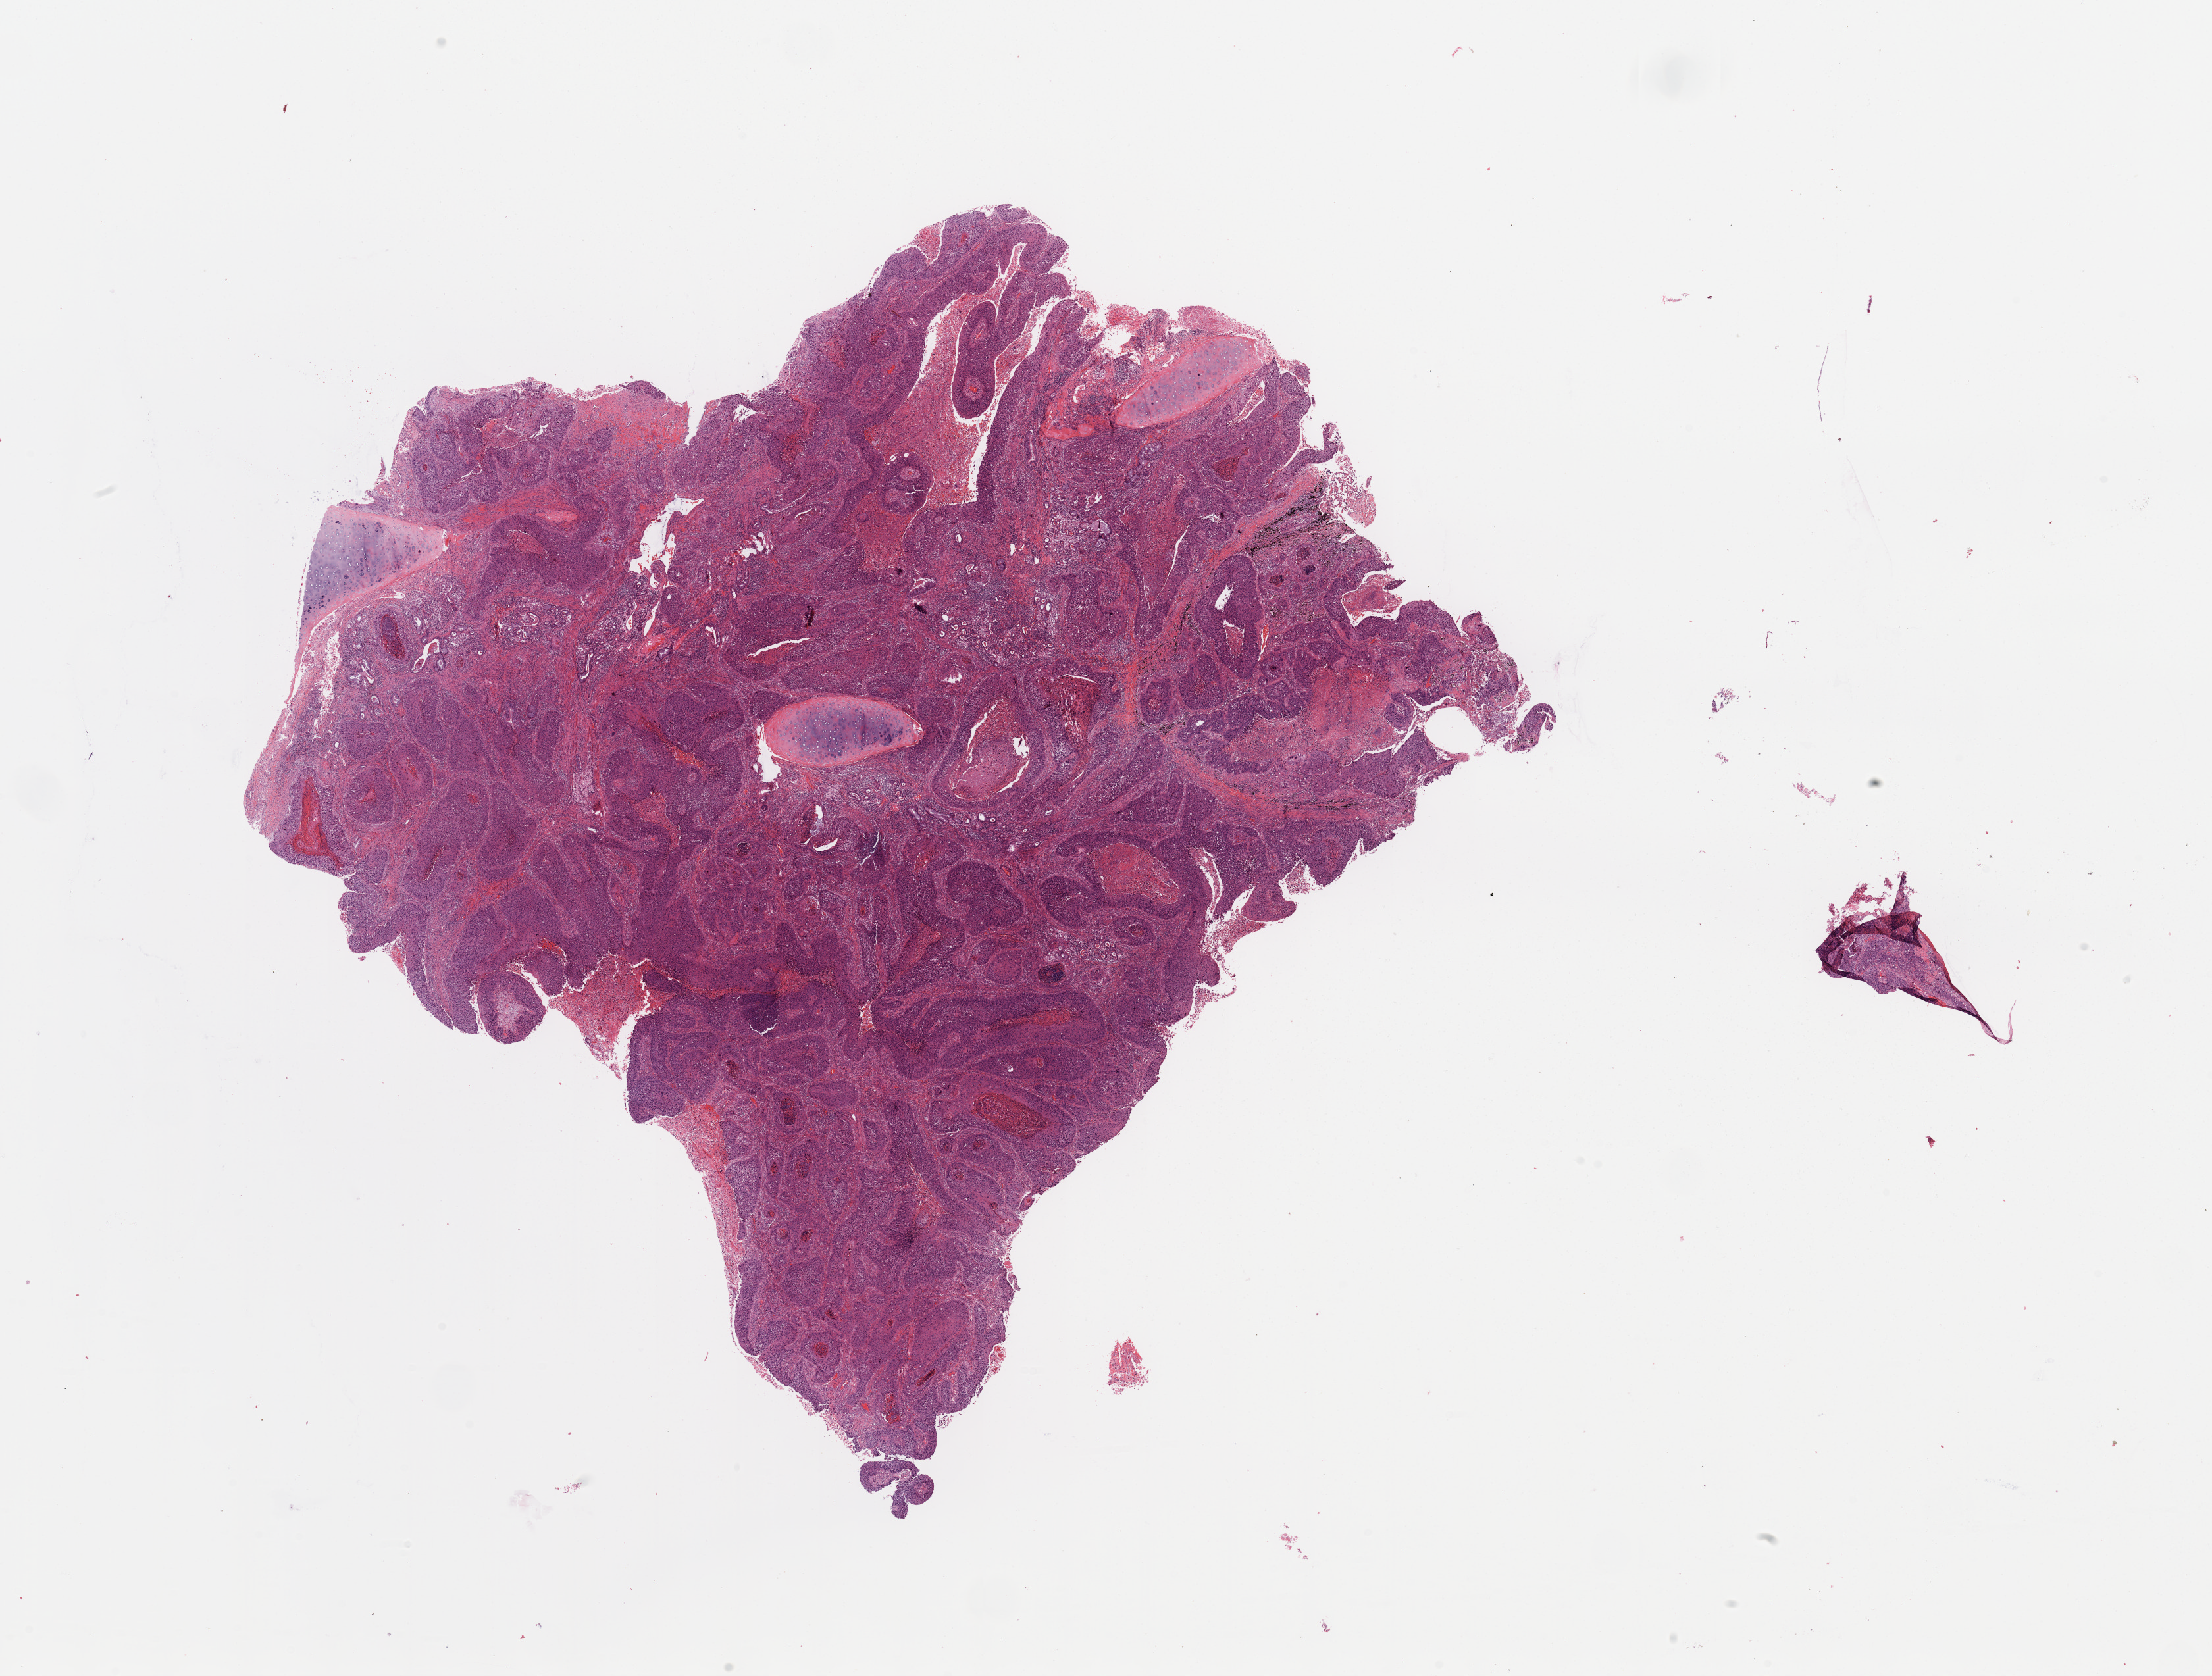
Digitized Hematoxylin and eosin (H&E) stained tissue section (whole slide), shown as a low-resolution overview of the whole scanned area (about 26.6 x 20.1 mm, from a 20x scan); tumour tissue sample, sampled site: lung. Male, 67 y/o. Histologic grade: G2 (moderately differentiated). Composition of this section per pathologist review: tumour nuclei 80%, necrosis 10%.
Diagnosis: Squamous cell carcinoma, NOS. AJCC pathologic stage: IIA.